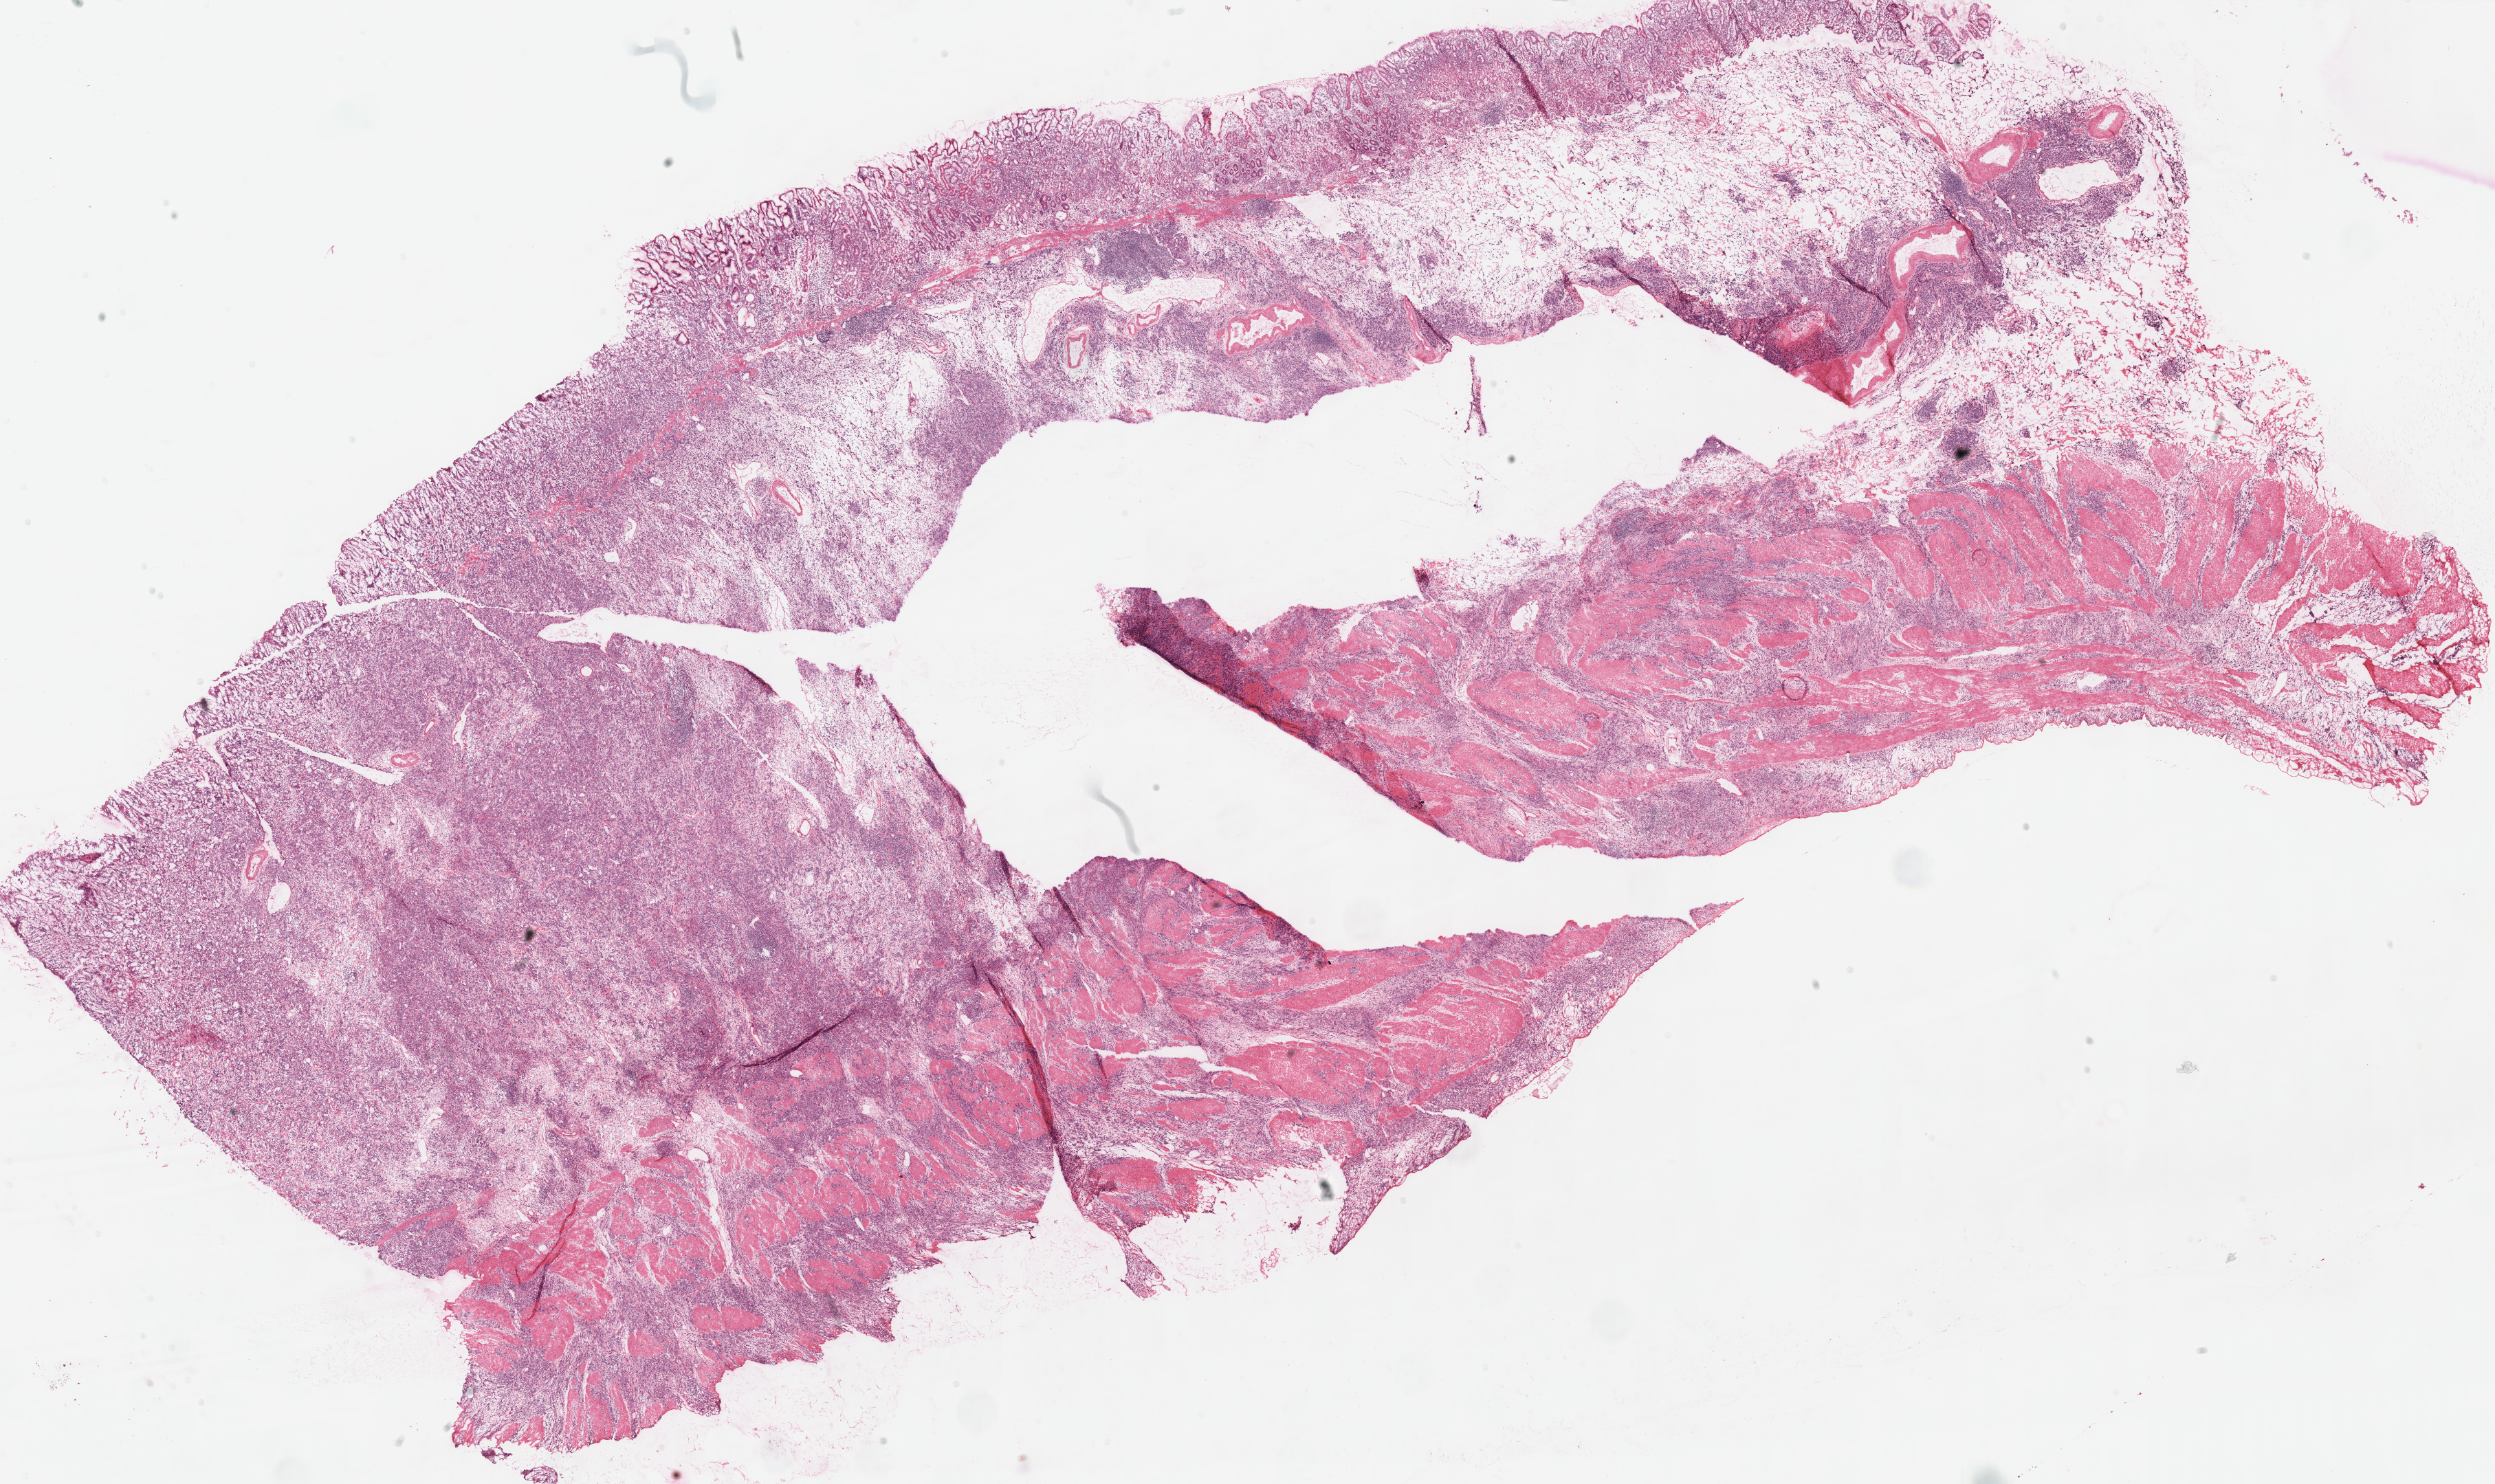
Digitized H&E tissue section (whole slide), shown as a low-resolution overview of the whole scanned area (about 28.6 x 17.0 mm, acquisition: 40x scan). Frozen section from the top of the tissue portion. Stomach, primary tumour sample. Patient: male, age at initial diagnosis 69 years. Histologic grade: G3 (poorly differentiated). Pathologist review of this section (percent, as recorded): tumour cells 90%, tumour nuclei 70%, normal cells 10%, stromal cells 0%, necrosis 0%. Inflammatory infiltration, as recorded: lymphocyte infiltration 15%, monocyte infiltration 0%, neutrophil infiltration 5%.
Histologic diagnosis: Tubular adenocarcinoma (gastric antrum). AJCC pathologic stage: IIIB.